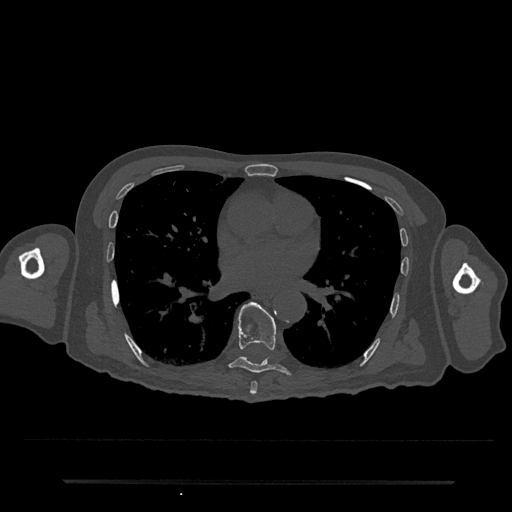
CT including the spine, one axial slice; slice 426 of 797 in the series (ordered by position); reconstruction kernel Br40s/3; bone window (W 1800 / L 400 HU); 0.5 mm slice thickness; 512 × 512 image matrix. Male patient, age 74 years. Case-level facts recorded for this patient, not image findings: primary cancer: prostate.
Outlined on this slice (semi-automatically segmented with operator editing):
- T7 vertebra: box from (x=250, y=382) to (x=258, y=395) px
- T8 vertebra: (x=228, y=302)–(x=291, y=376)